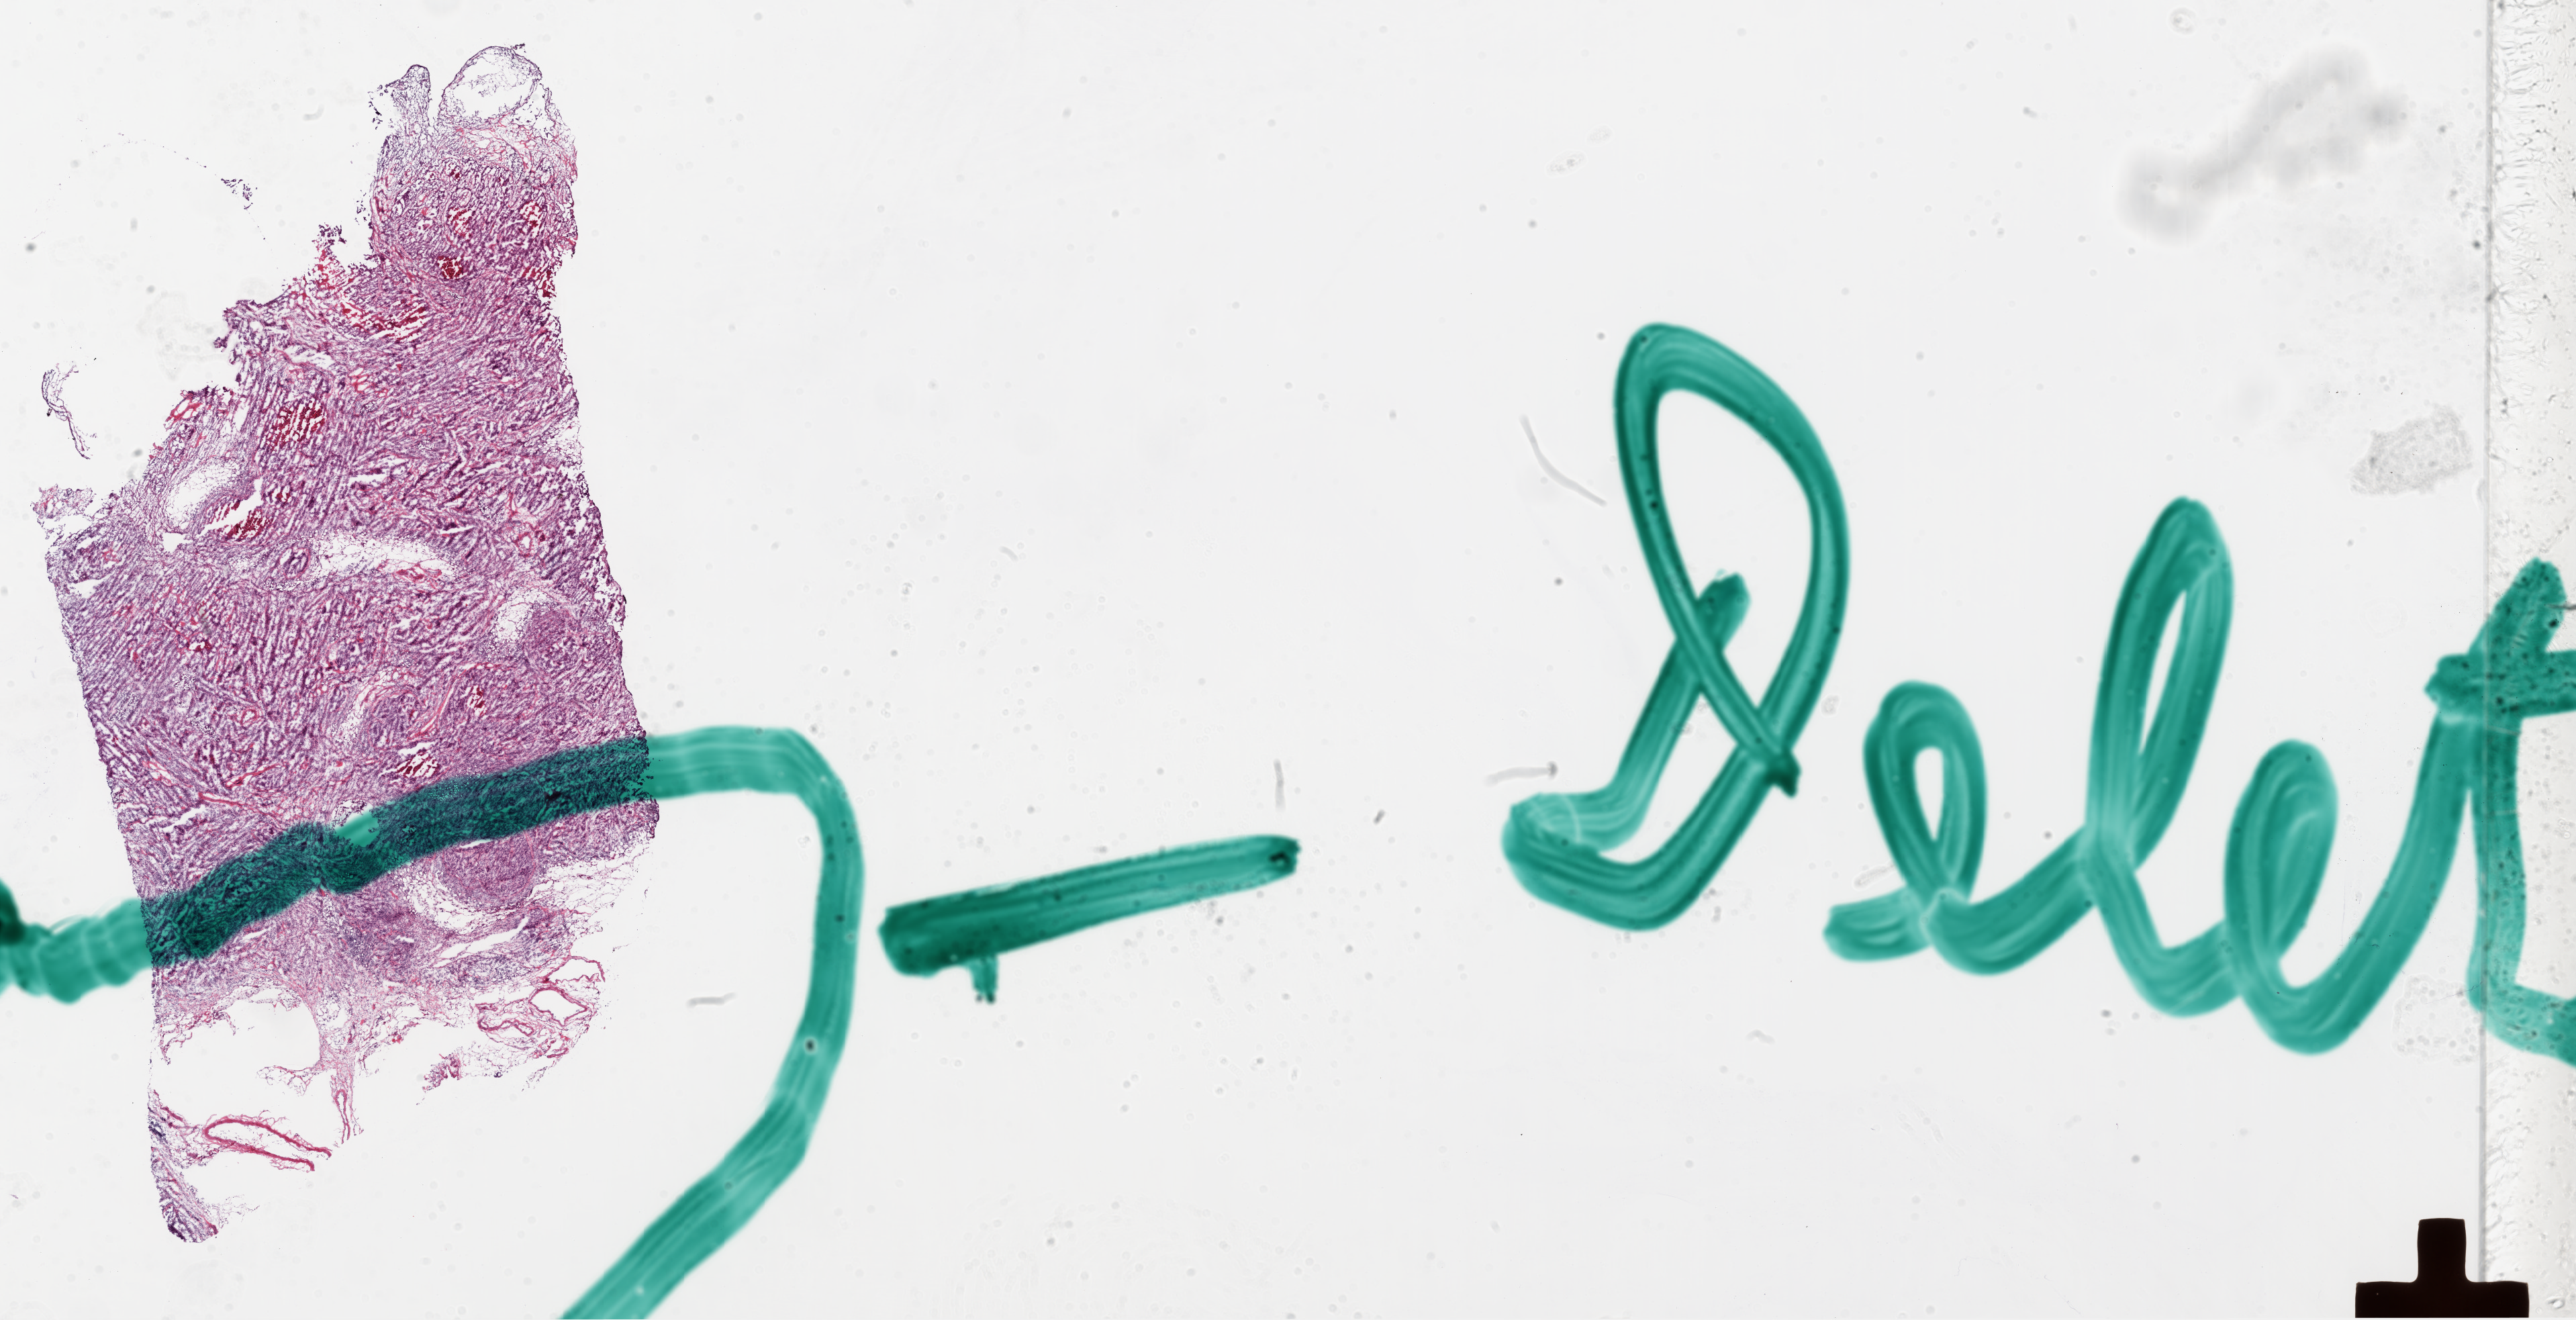
Whole-slide histology image, Hematoxylin and eosin (H&E) stained, a low-resolution overview of the entire scanned area, about 30.9 x 15.9 mm; frozen section; primary tumour sample from the ovary. Female patient; age at initial diagnosis 73 years. Pathologist review of this section (percent, as recorded): tumour cells 89%, tumour nuclei 90%.
Pathologic diagnosis: Serous cystadenocarcinoma, NOS.